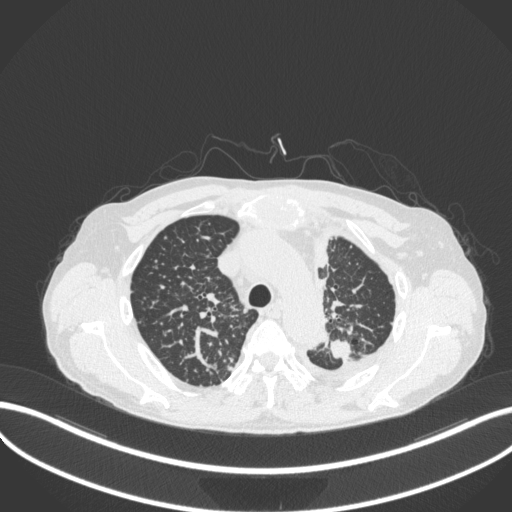
Chest CT, one axial slice; position 269 of 319 along the scan axis; 120 kVp; lung window (W 1500 / L -600 HU); 1 mm slice thickness; 512 × 512 image matrix. Patient: male, 58 years. Case-level facts recorded for this patient, not image findings: clinical TNM (as recorded): T1c N3 M1.
Outlined on this slice (rectangle marked by the reading radiologist):
- lung tumour (recorded histology: adenocarcinoma): bounding box <327,336,360,363> (left, top, right, bottom; pixels)